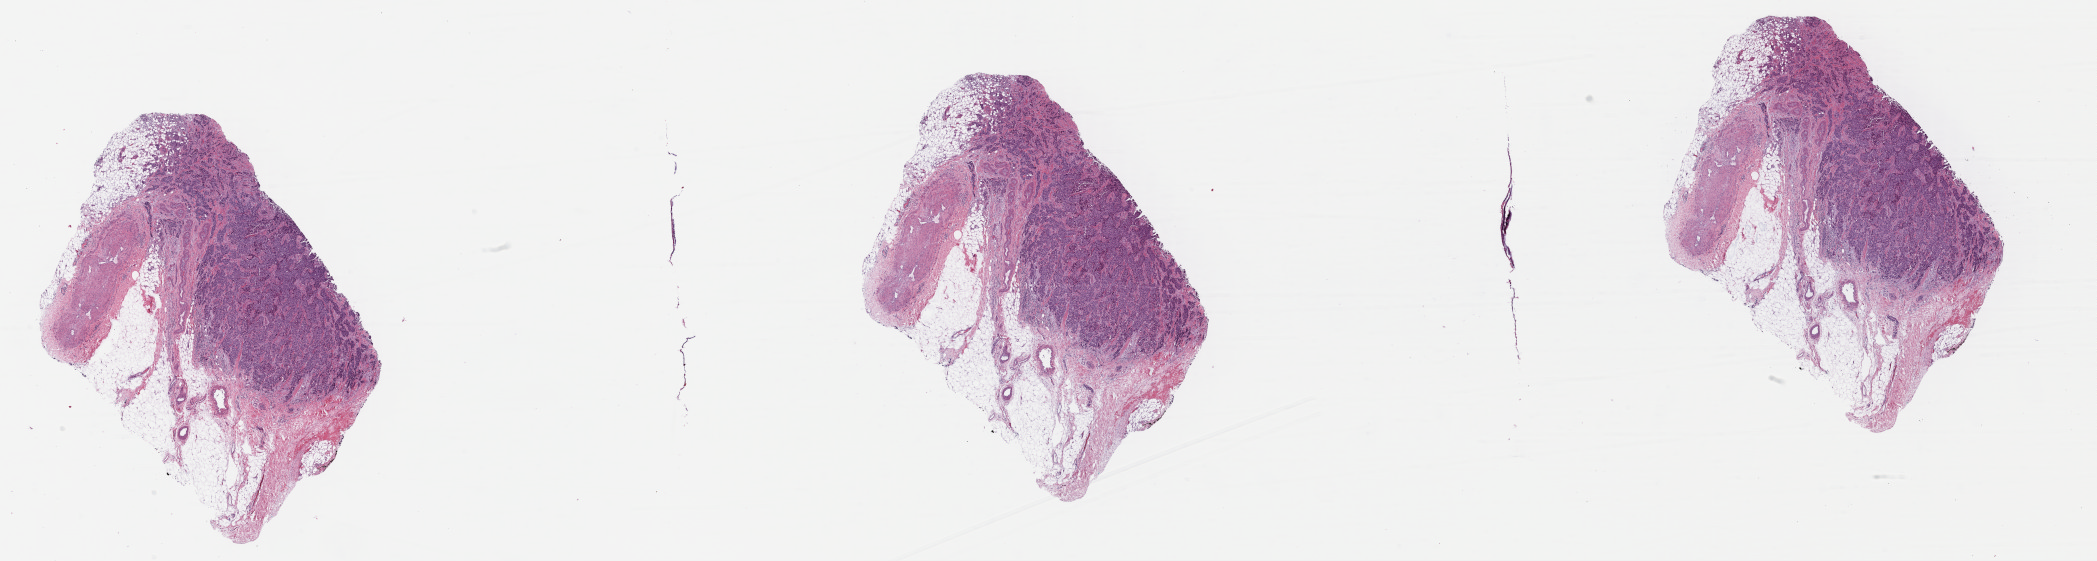
Digitized H&E tissue section (whole slide), whole scanned area (about 33.0 x 8.8 mm, from a 40x scan) shown as a low-resolution overview. Formalin-fixed paraffin-embedded (FFPE) diagnostic section. Sample: primary tumour, breast. Patient: female, age at initial diagnosis 68 years.
TNM: T2 N0 M0. Histologic diagnosis: Infiltrating duct carcinoma, NOS. AJCC pathologic stage: IIA (7th edition). Lymph nodes positive (case pathology): 0 of 2 examined. Laterality: left.